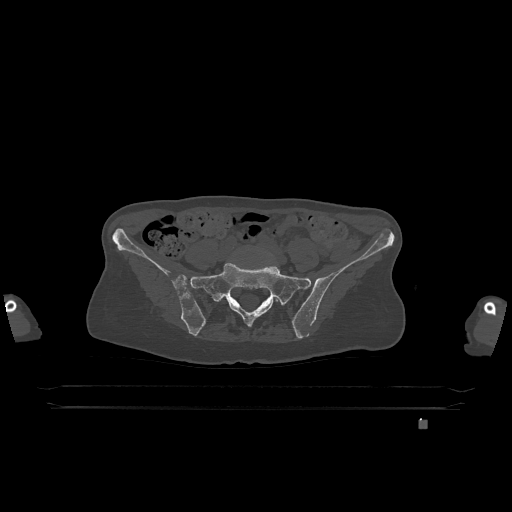
CT including the spine, one axial slice; slice 196 of 1317 in the series (ordered by position); bone window (W 1800 / L 400 HU); 0.5 mm slice thickness; 512 × 512 image matrix, field of view 500 × 500 mm. Female patient, age 74 years. Case-level facts recorded for this patient, not image findings: primary cancer: lung.
Annotated regions visible in this slice (semi-automatic segmentation, software-assisted and operator-edited):
- L5 vertebra: bounding box (x1, y1, x2, y2) in pixels: (275, 299, 278, 302)